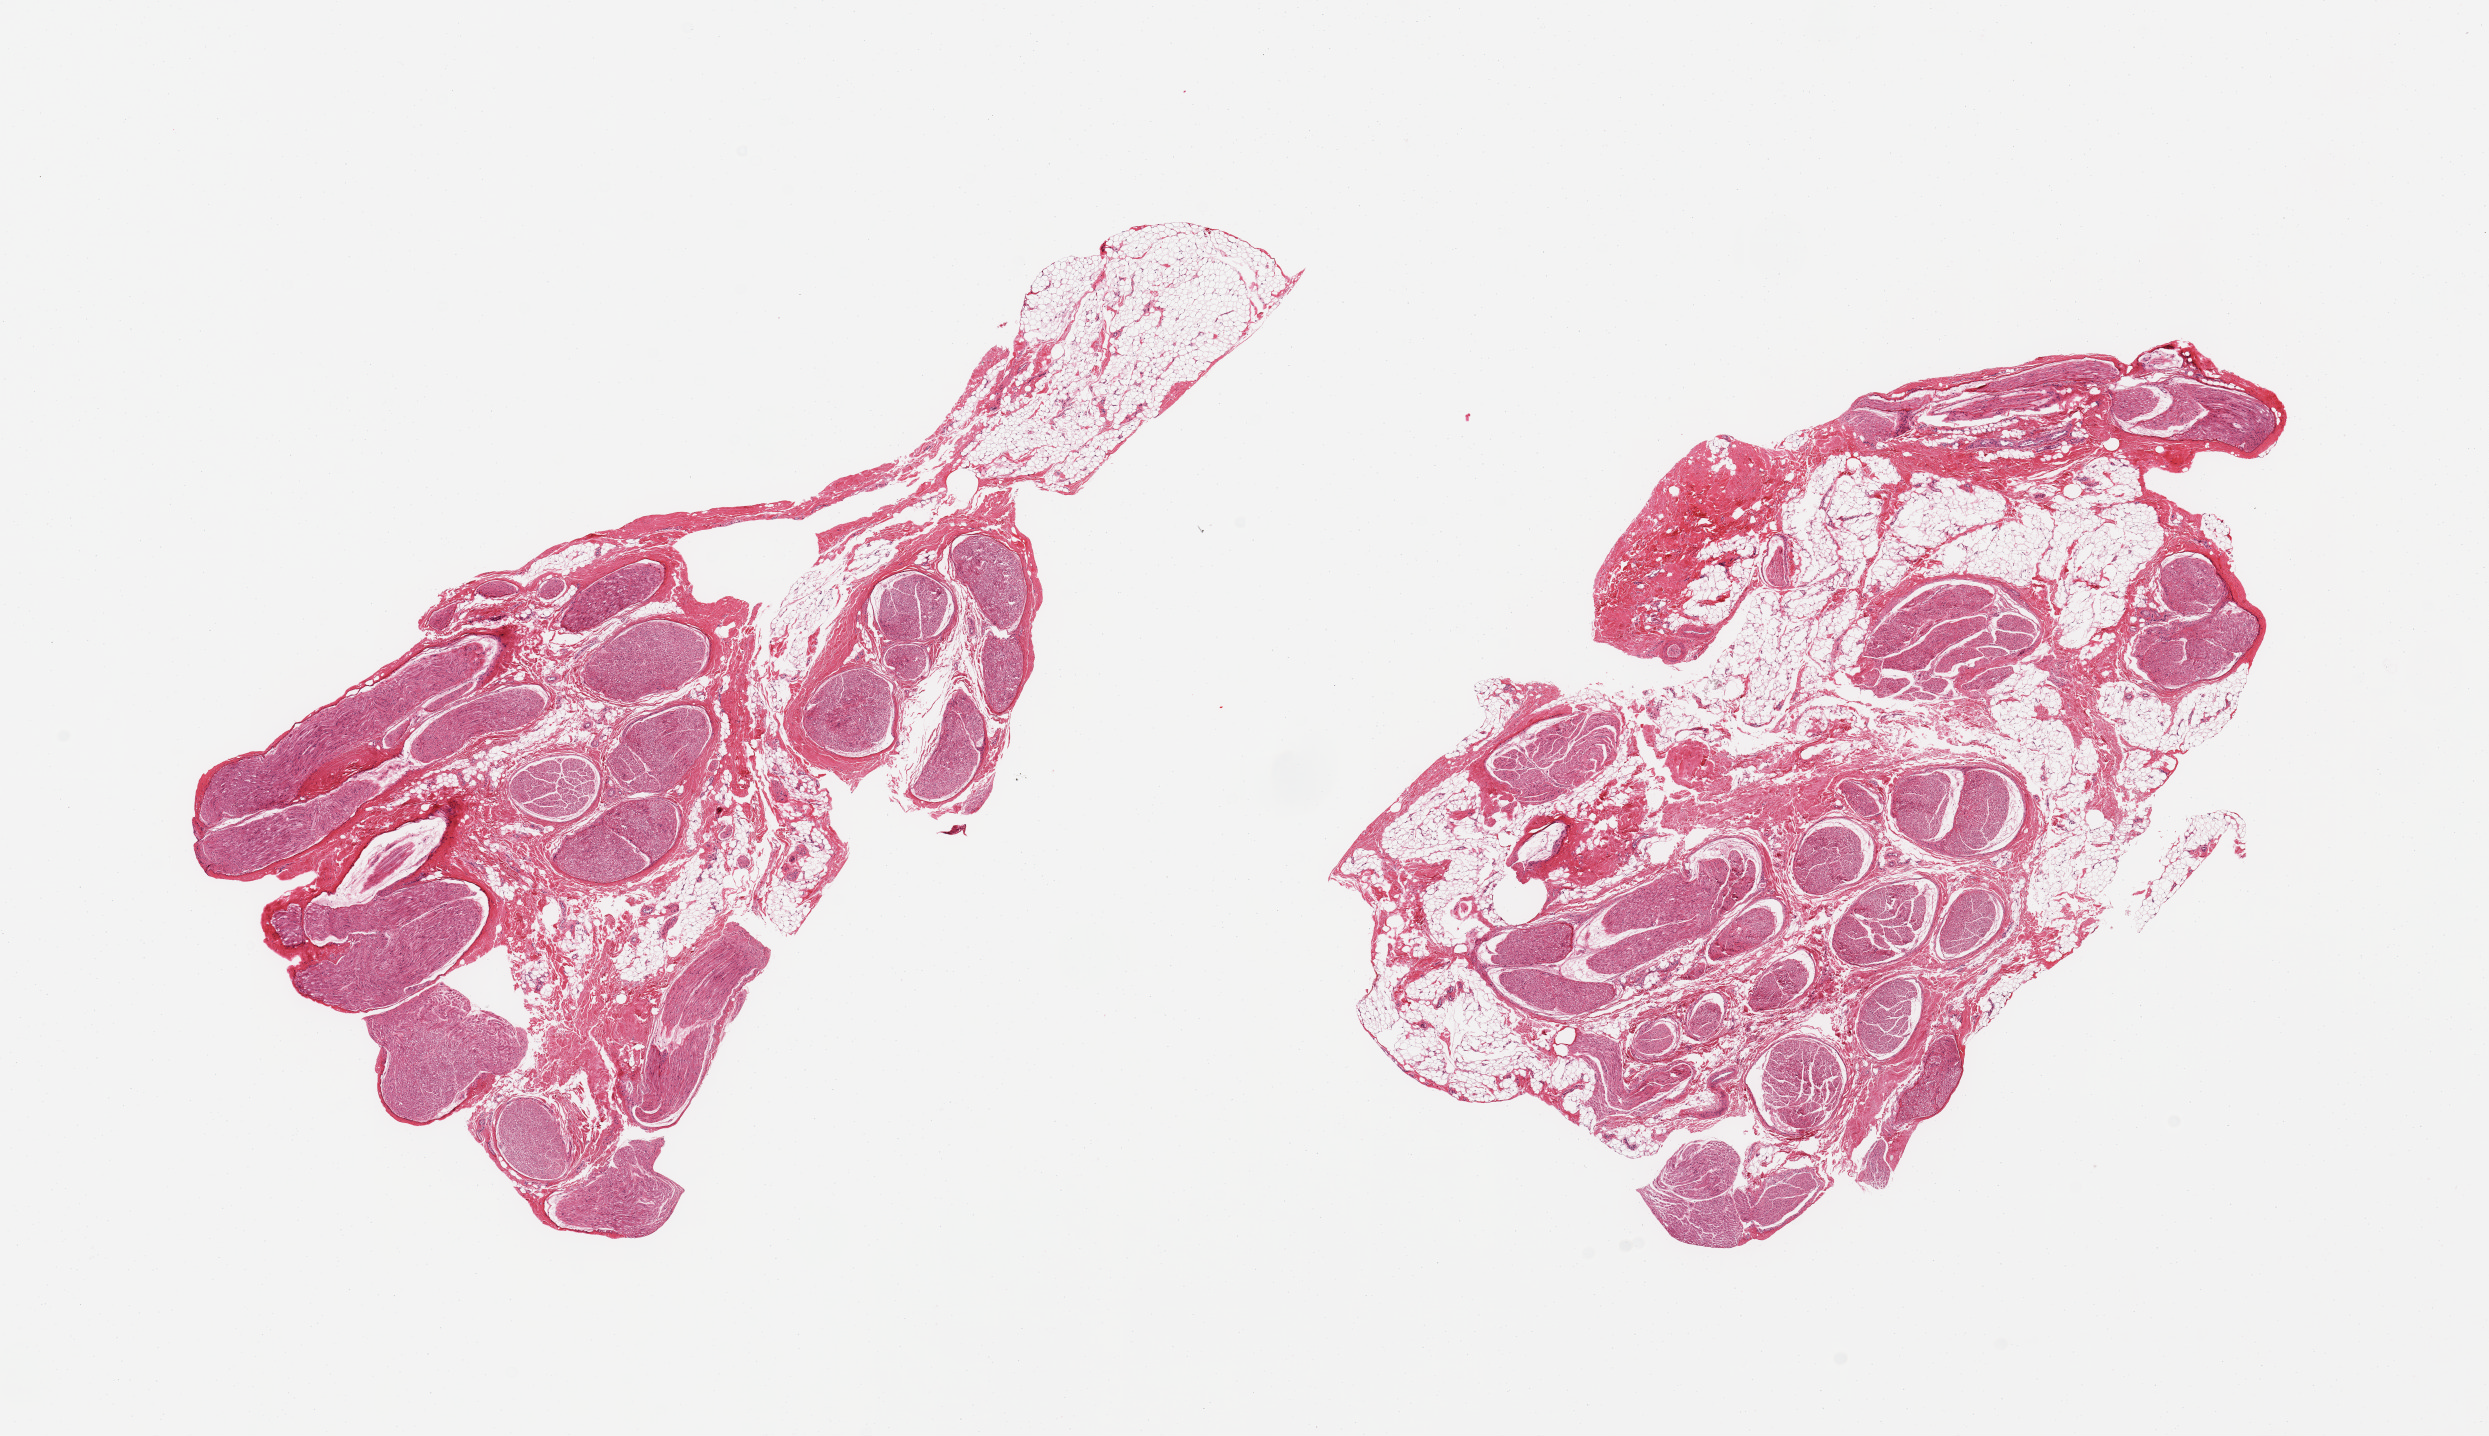
Haematoxylin and eosin whole-slide image — shown as a low-resolution overview of the whole scanned area (about 19.7 x 11.4 mm), PAXgene-fixed, paraffin-embedded tissue, section of tibial nerve (target tissue), donor tissue sample. Male donor.
- review note (as recorded): 2 pieces, nerve is ~70% of specimen rest is adherent/interstitial fat